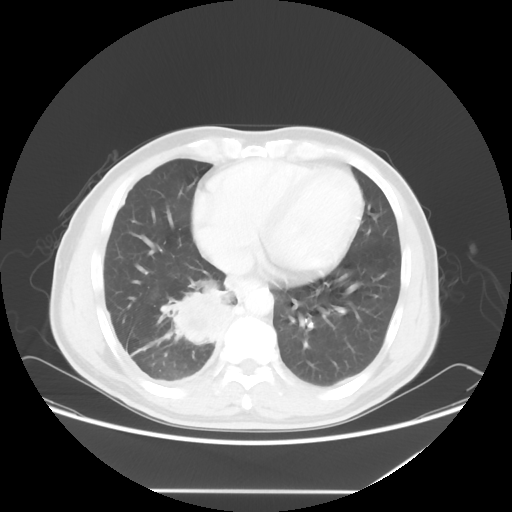
Chest CT, one axial slice; slice 22 of 60 in the series (ordered by position); lung window (W 1500 / L -600 HU); 5 mm slice thickness; 512 × 512 image matrix, field of view 419 × 419 mm. Male patient, age 48 years. From the clinical record (not read from this slice): clinical TNM (as recorded): T3 N3 M1a.
Annotated regions visible in this slice (rectangle marked by the reading radiologist):
- lung tumour (recorded histology: squamous cell carcinoma): box from (x=156, y=282) to (x=237, y=349) px